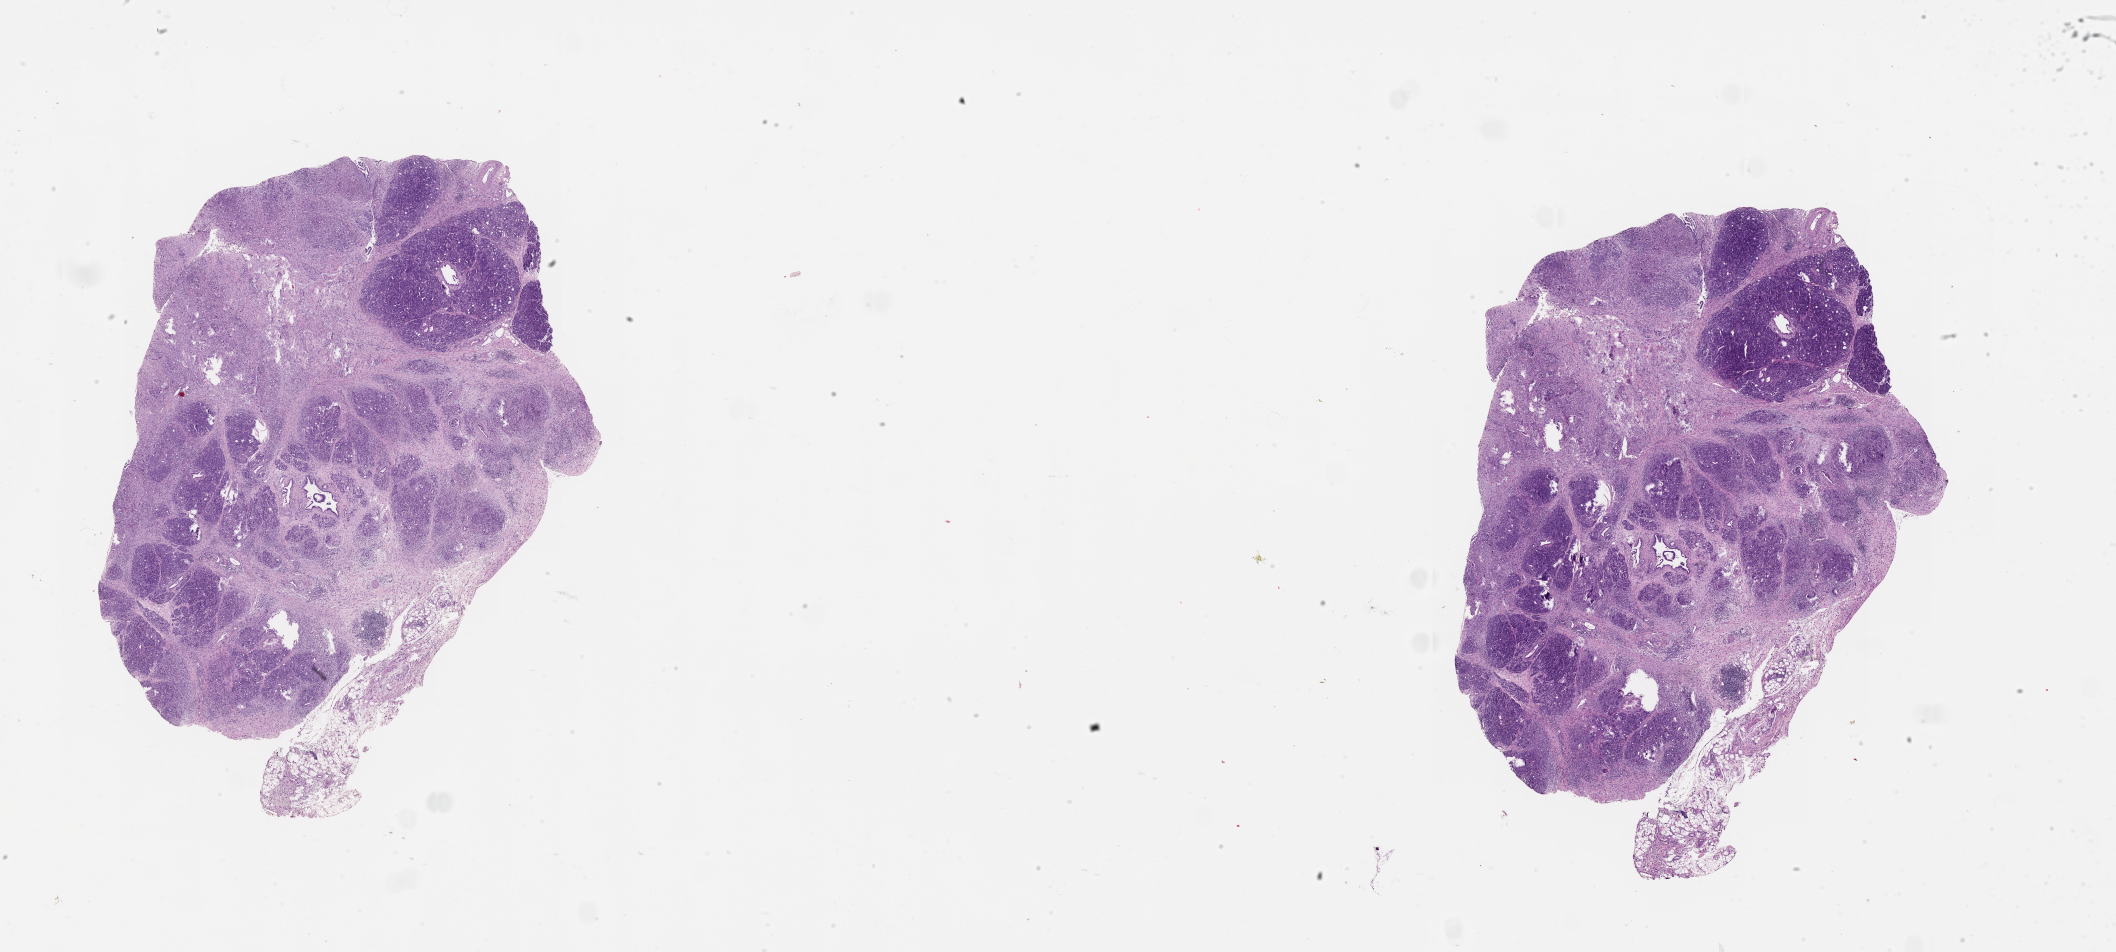
Whole-slide histology image, H&E, a low-resolution overview of the entire scanned area, about 34.1 x 15.3 mm (acquisition: 20x scan), tumour tissue sample, pancreas. 69-year-old male patient.
Histologic diagnosis: Infiltrating duct carcinoma, NOS.